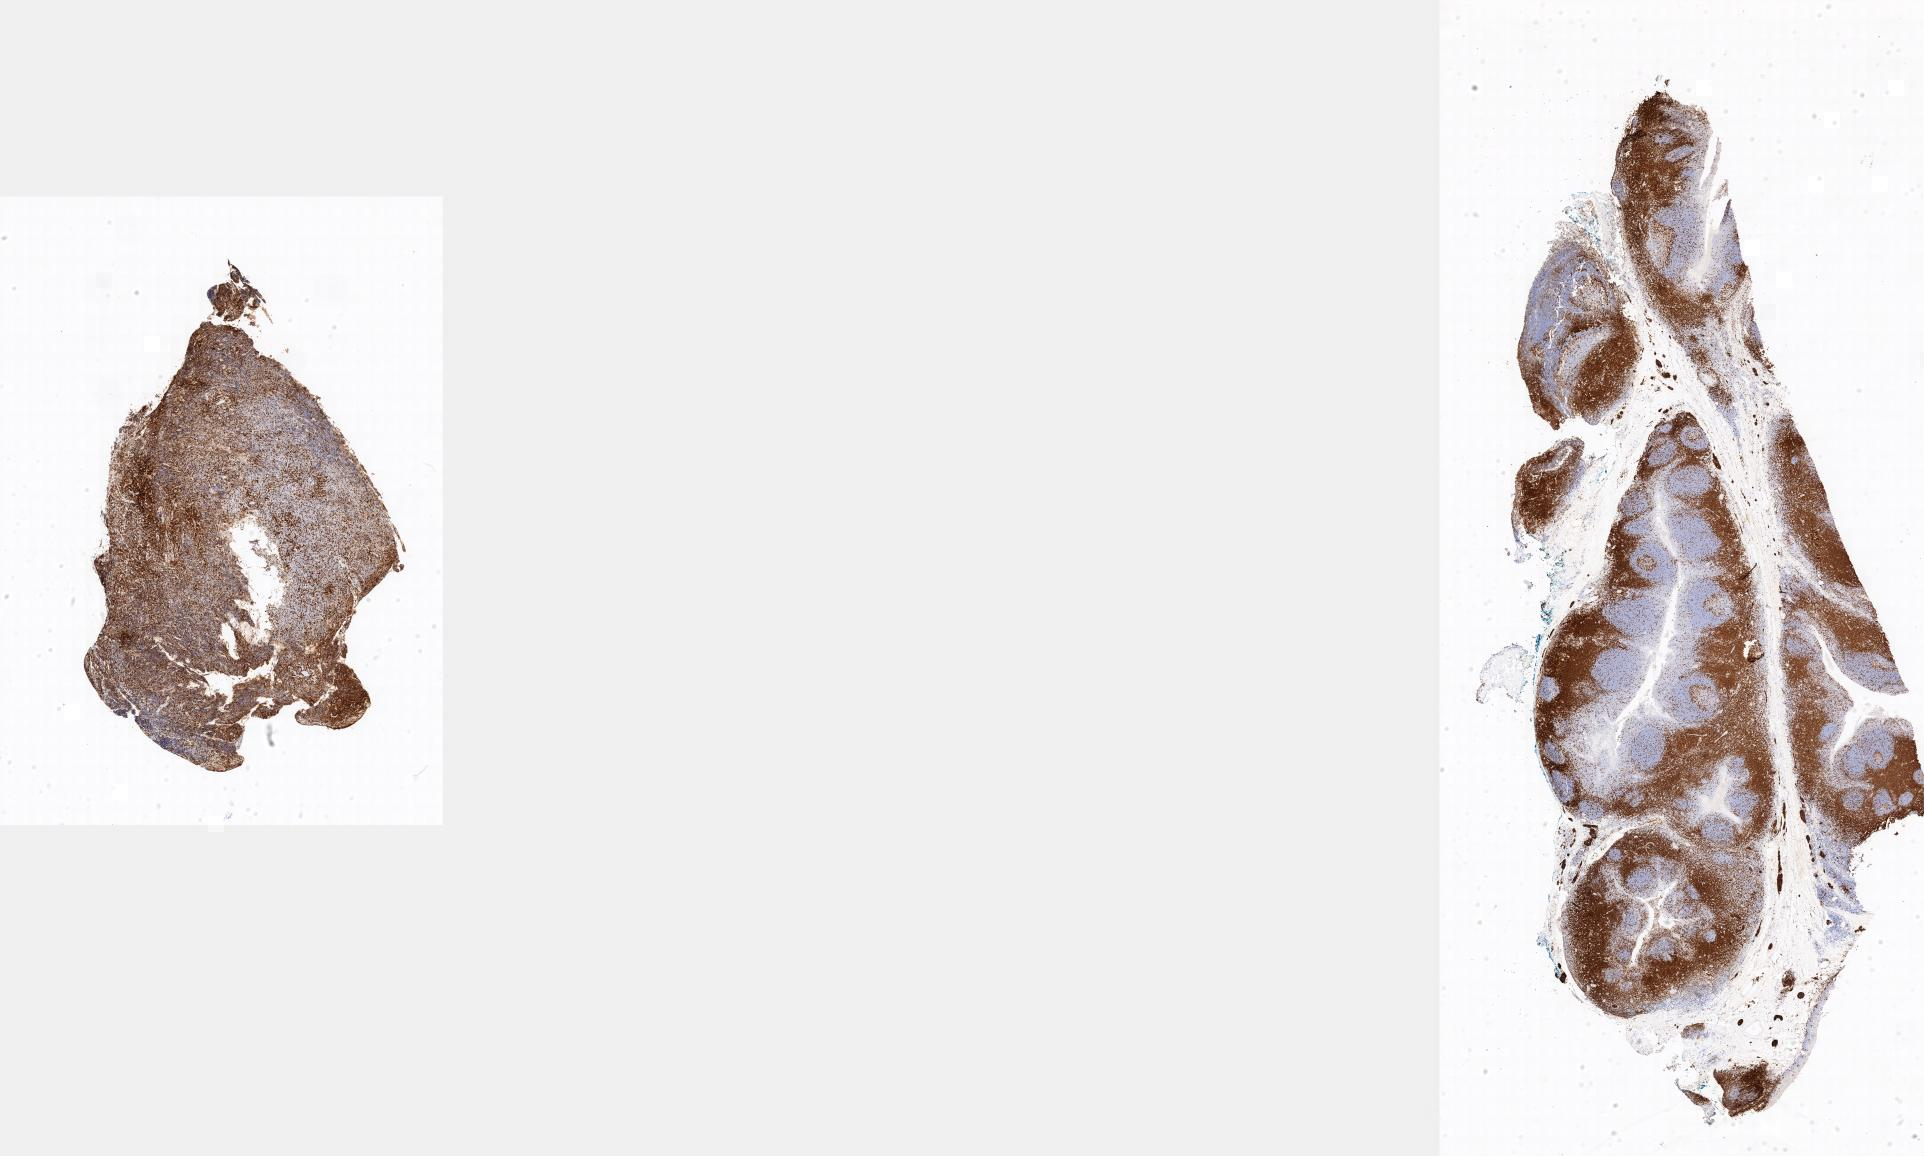
Immunohistochemistry (IHC) whole-slide image stained for CD3, a low-resolution overview of the entire scanned area. Specimen: tumor tissue. Site: ovary. Patient: female, age at initial diagnosis 3 years.
Diagnosis: Burkitt lymphoma, NOS.